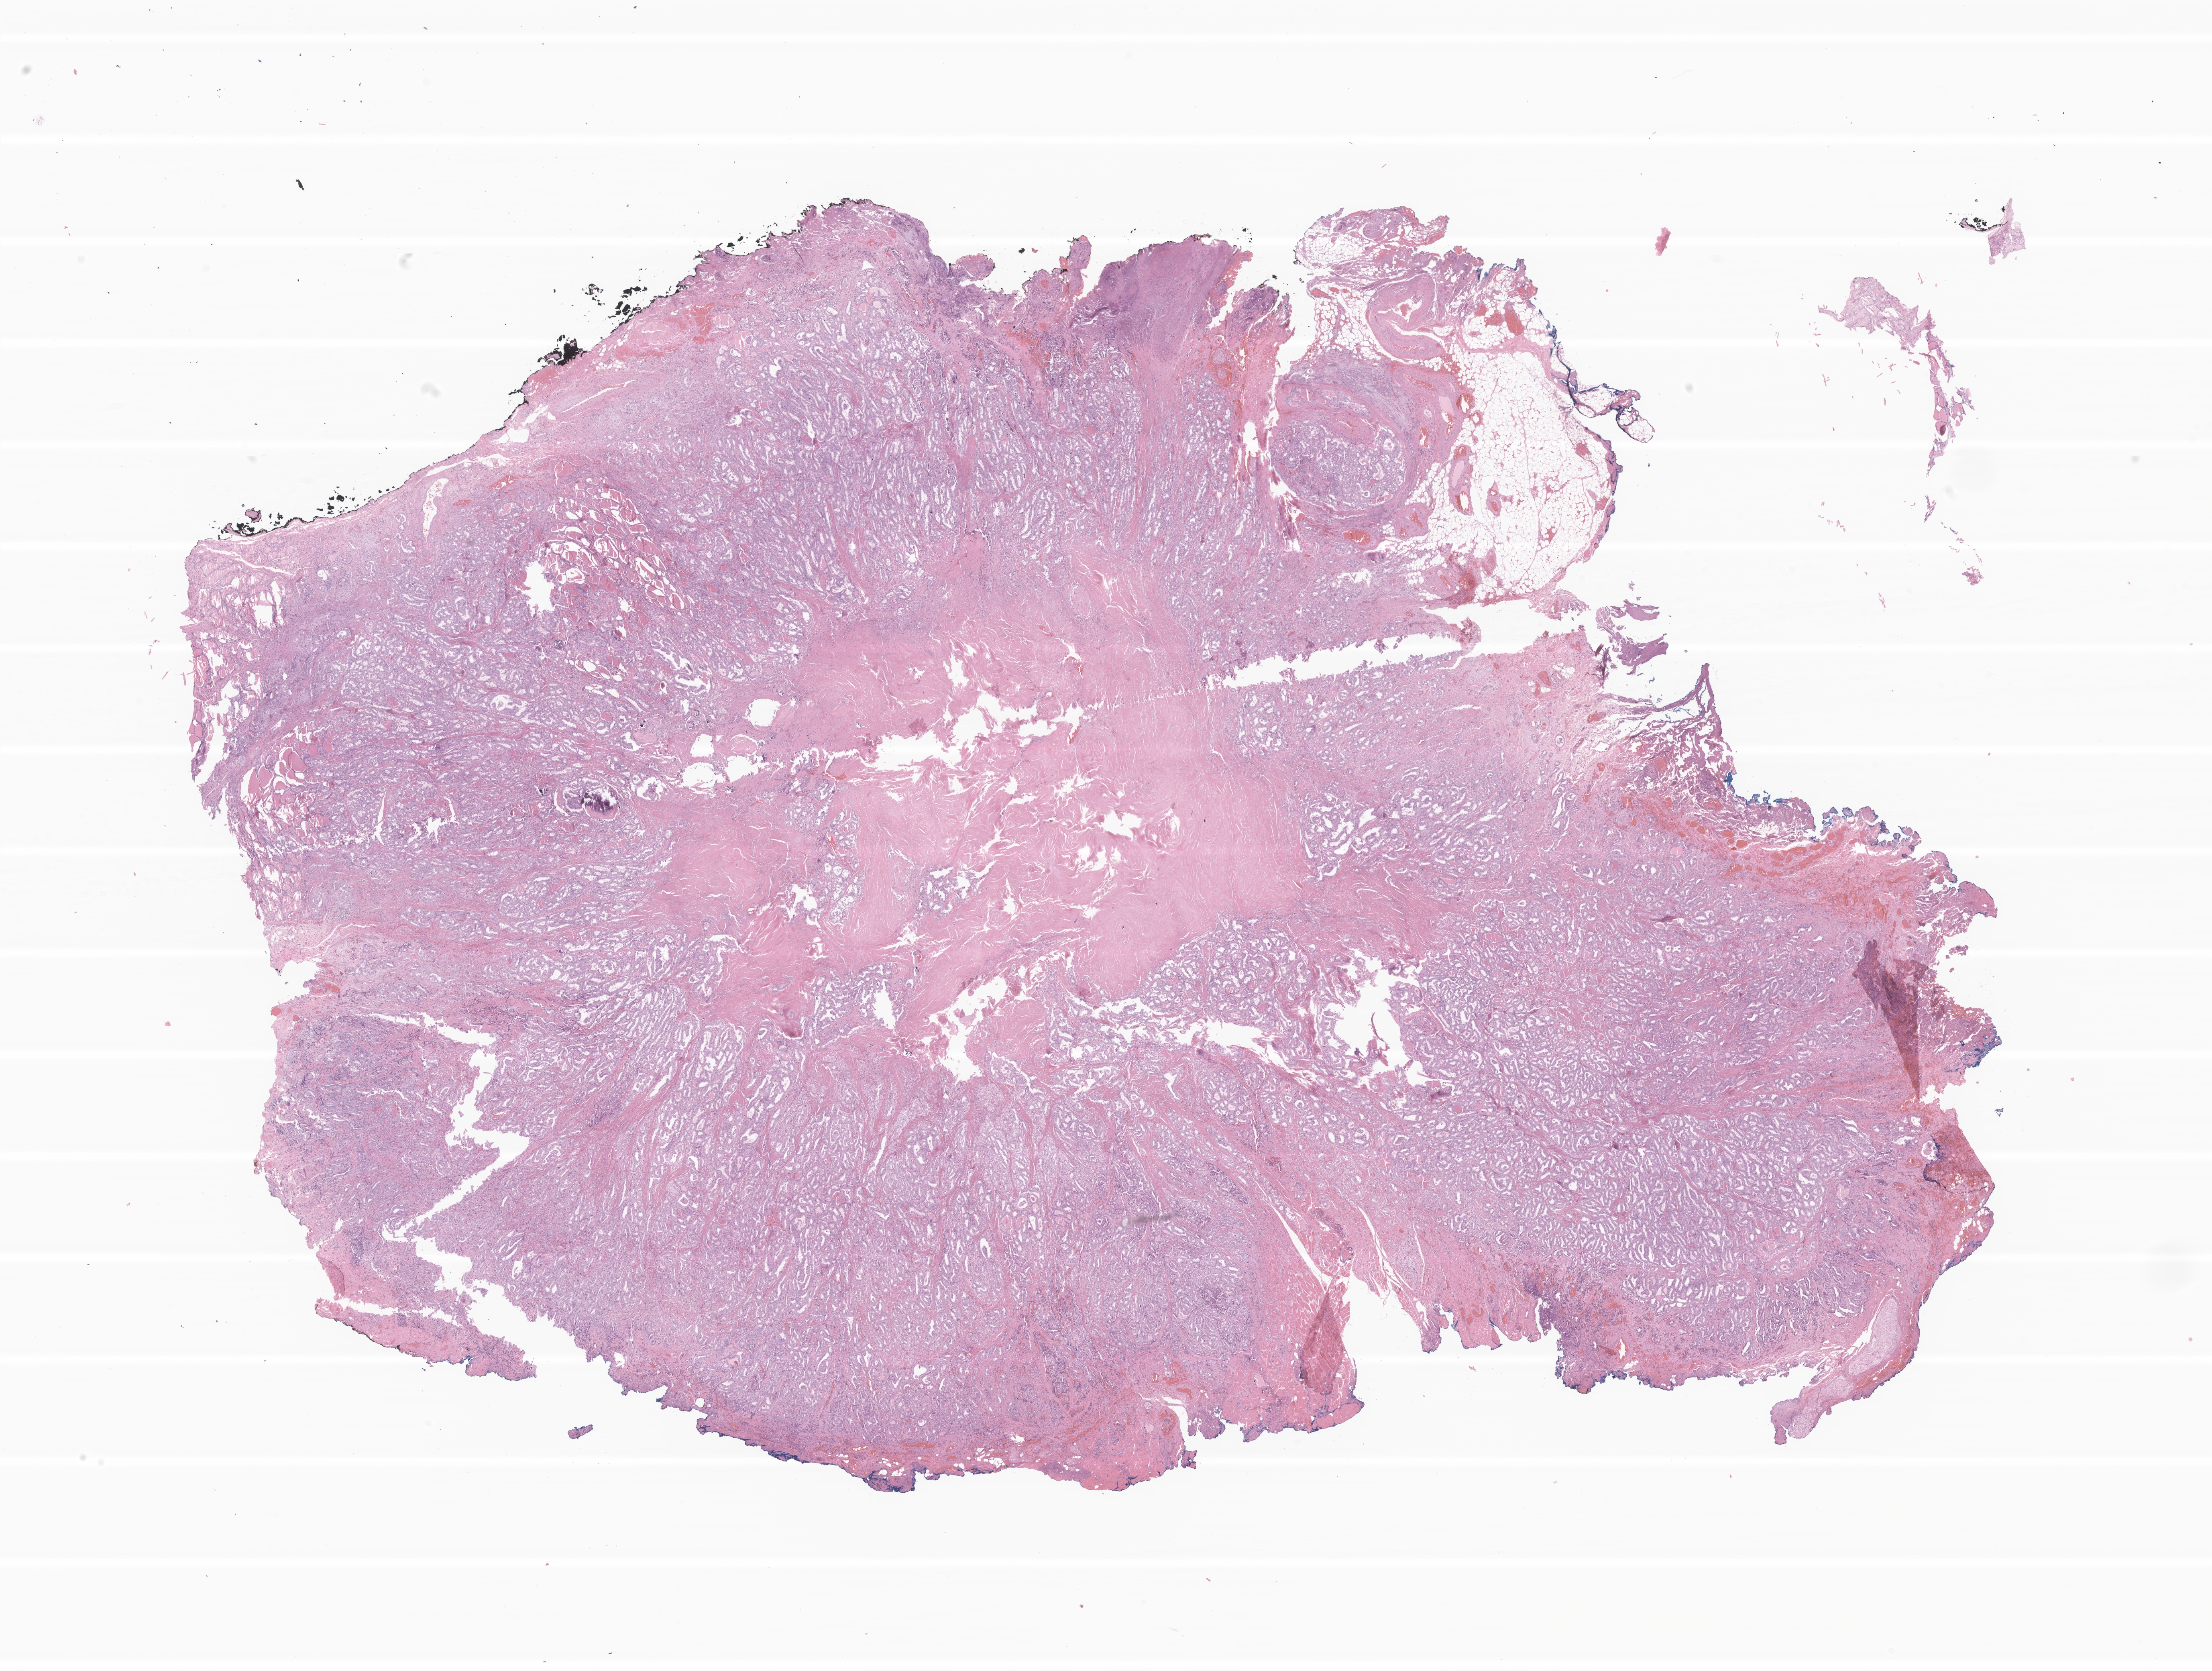
Digitized H&E-stained section of tumor tissue from the thyroid — a low-resolution overview of the entire scanned area, about 23.2 x 17.5 mm; formalin-fixed paraffin-embedded section. Patient female; age 191 months (15 years 11 months).
Diagnosis: Papillary carcinoma, NOS.